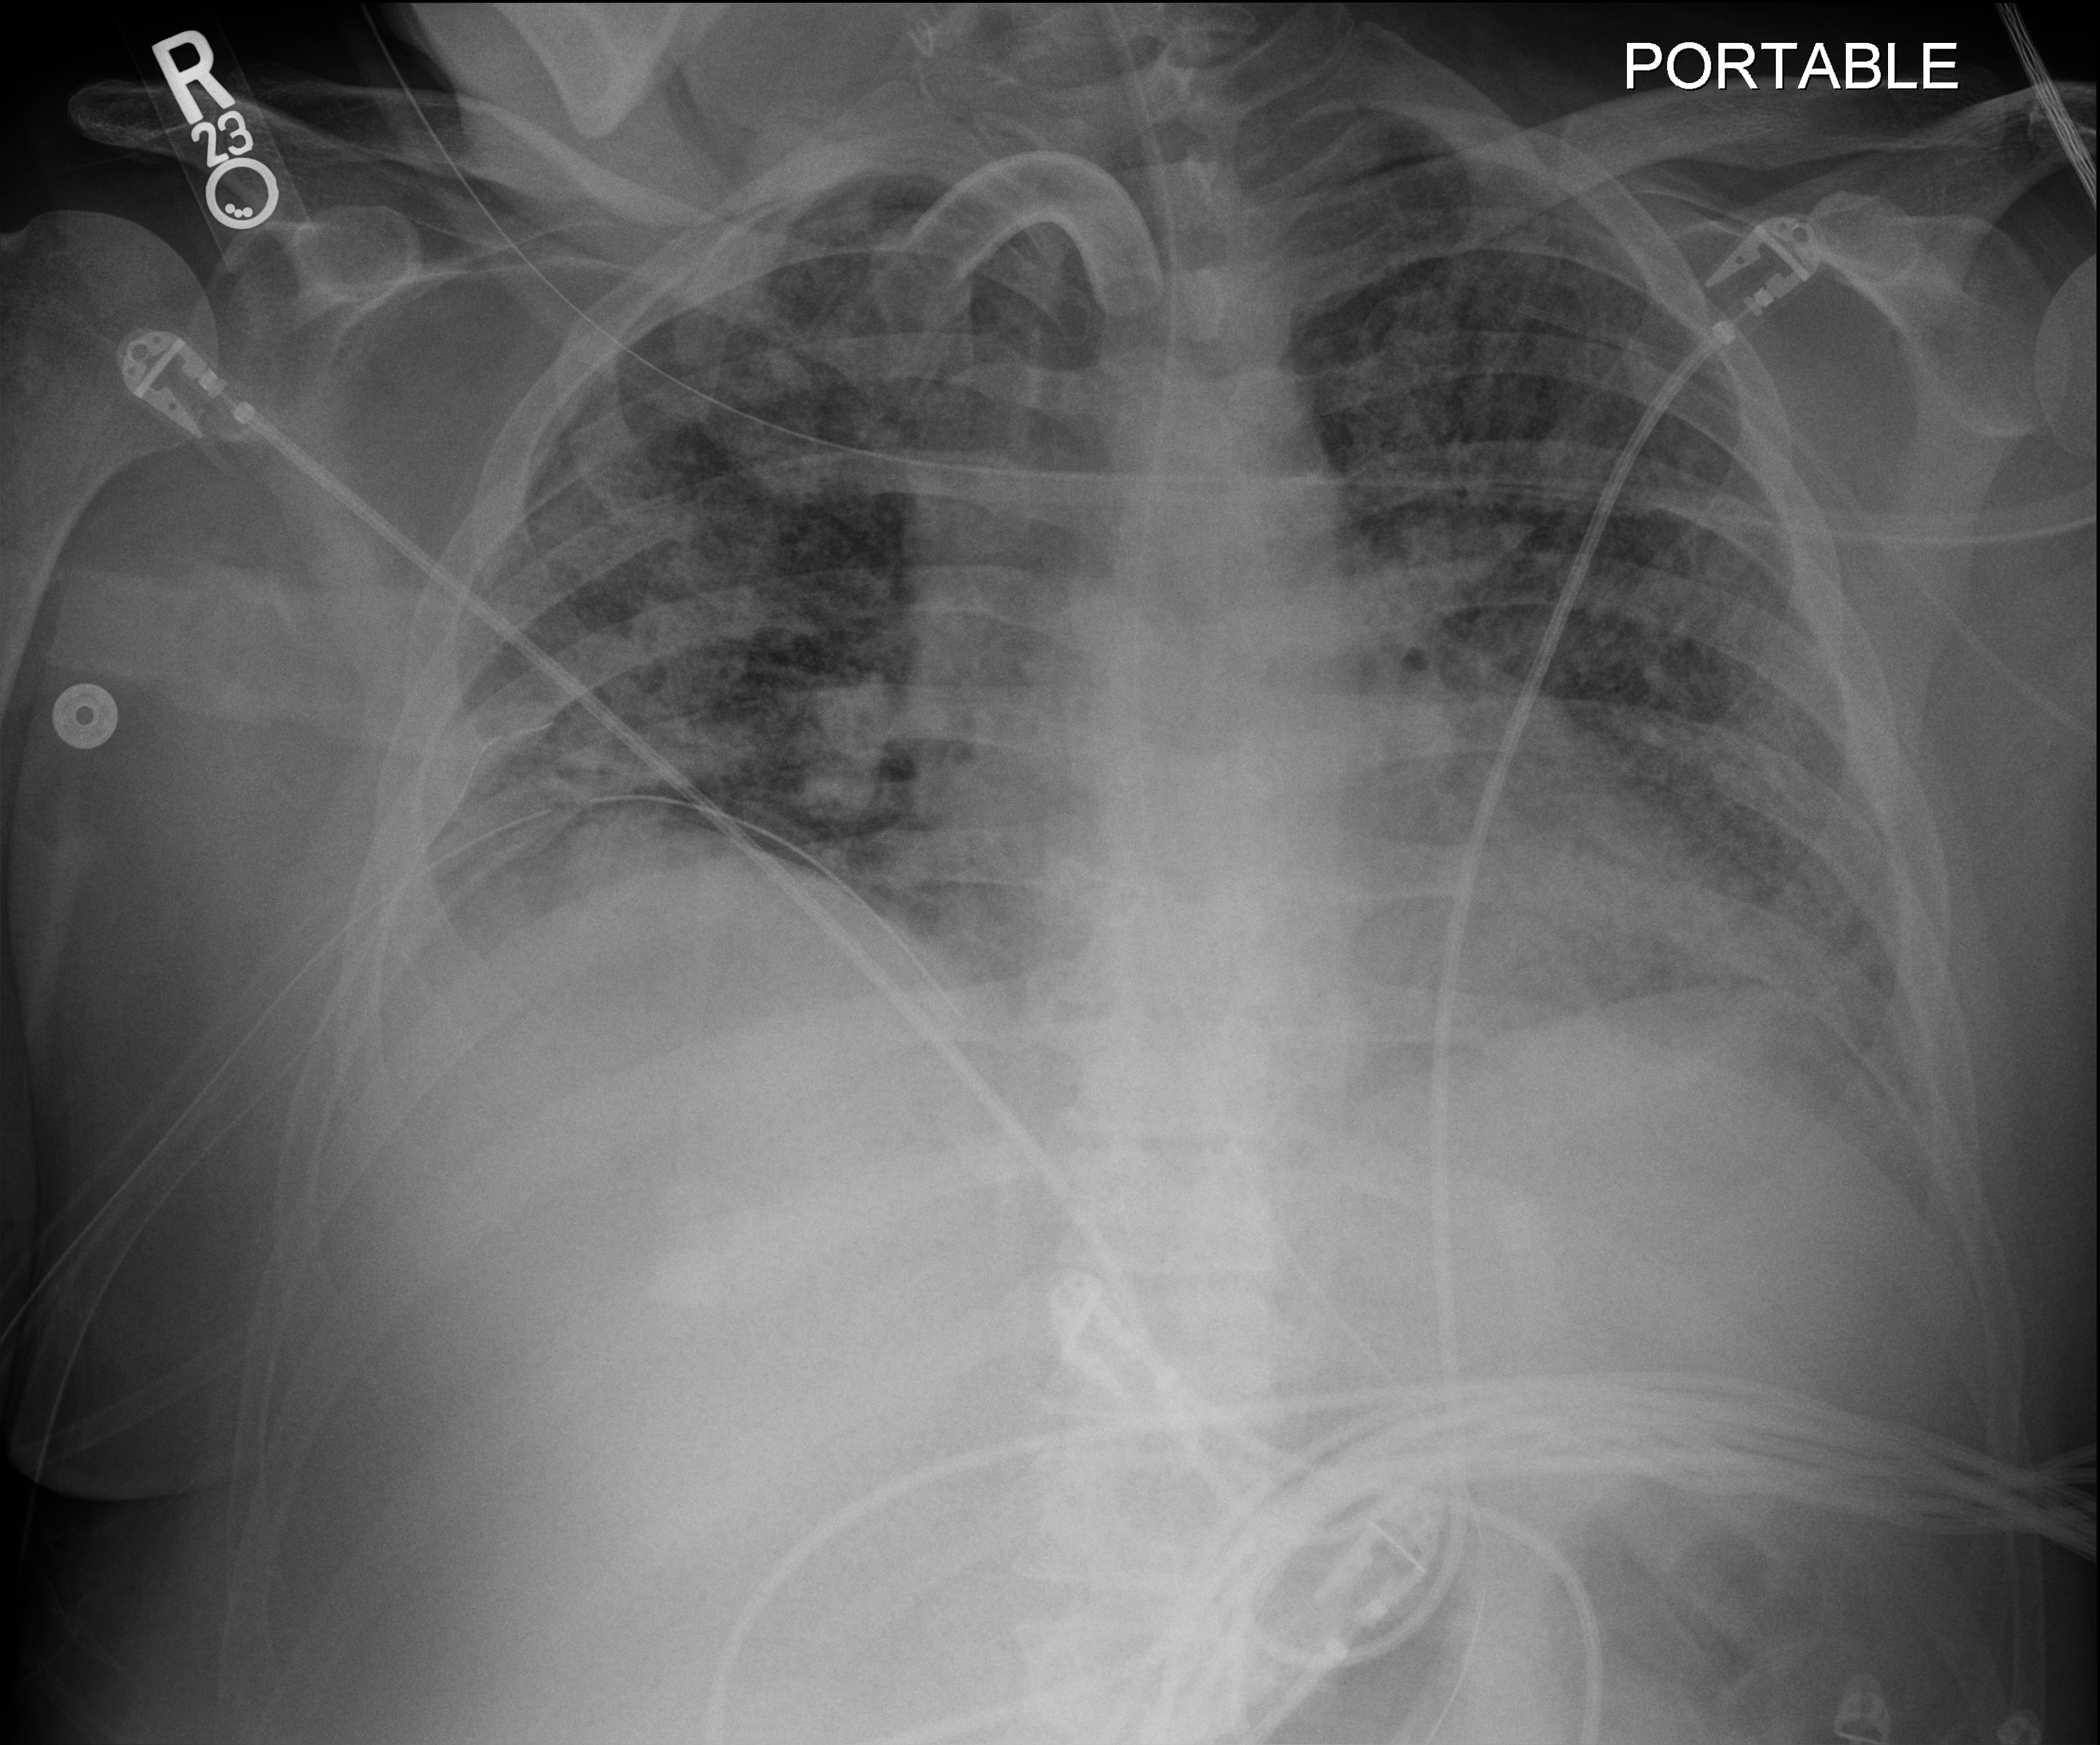
Portable chest radiograph, anteroposterior (AP) projection. Male patient hospitalised with COVID-19, age 18–59 years.
Admission-level facts for this patient (not findings on this image; timing relative to this image not recorded): chronic kidney disease (admission record): no; admitted to intensive care during this hospital stay: yes; mechanically ventilated during this hospital stay: yes.